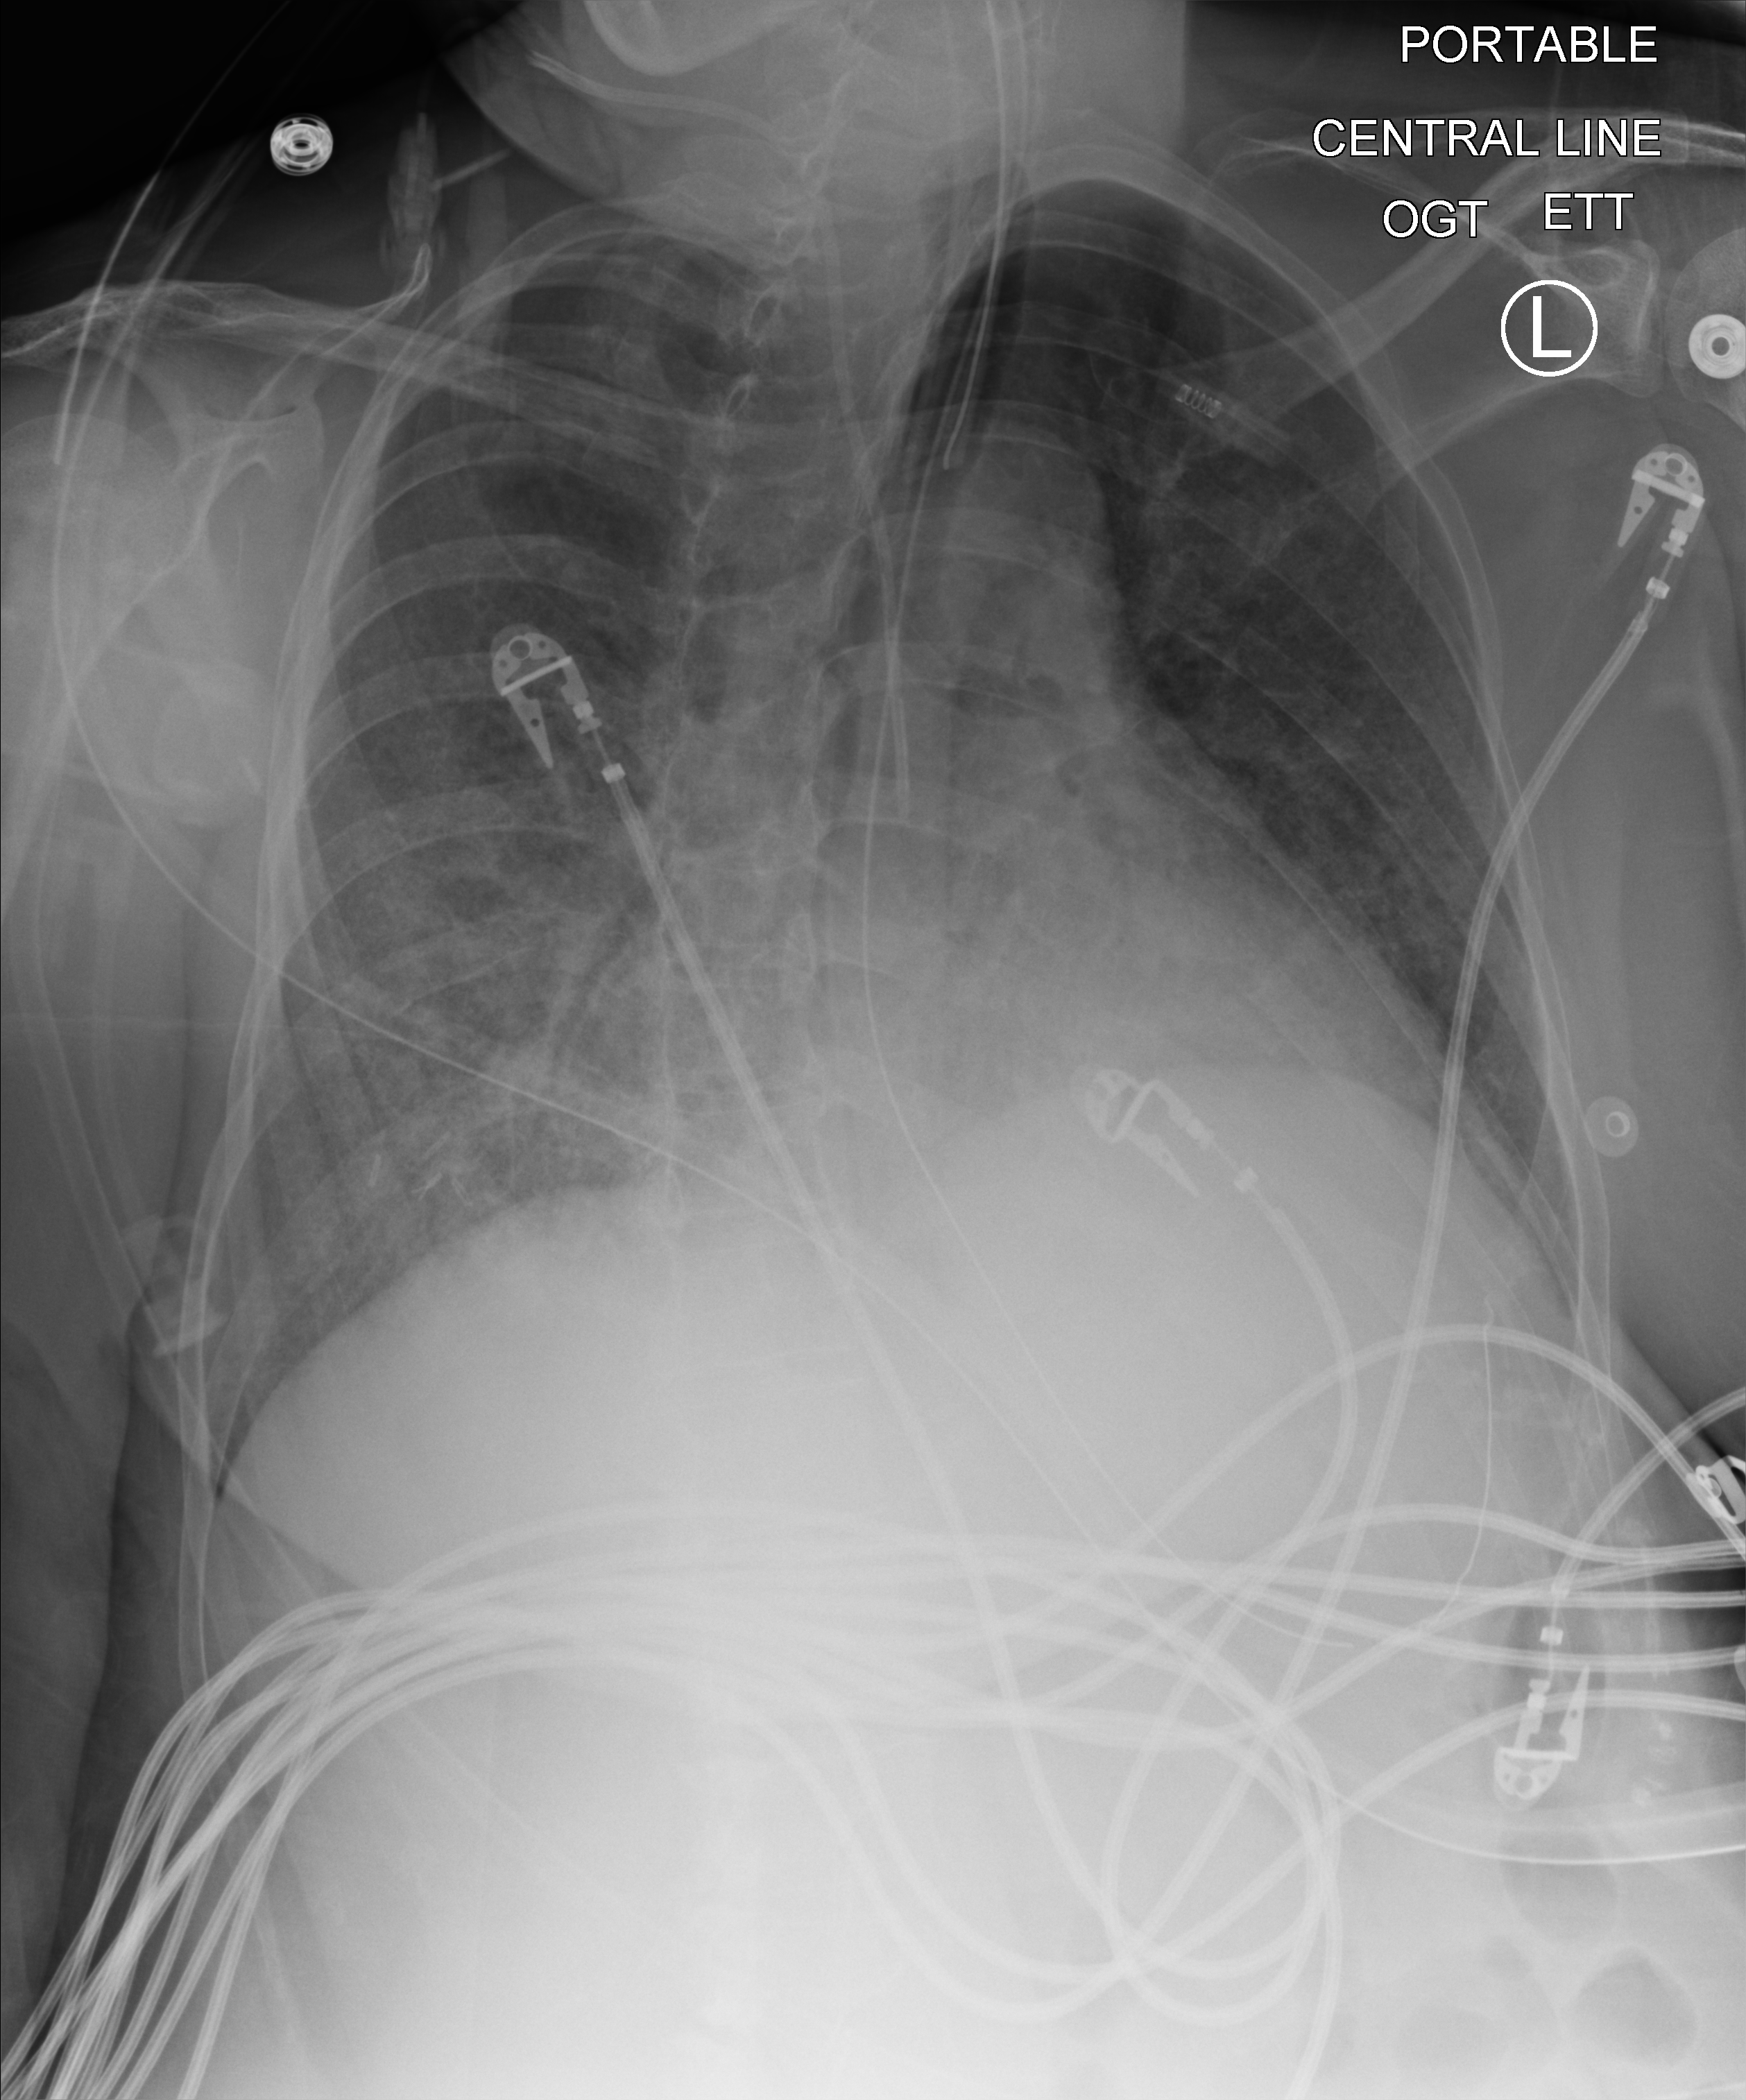
Bedside chest radiograph (computed radiography); anteroposterior (AP) projection. Female patient hospitalised with COVID-19, age 18–59 years.
Admission-level facts for this patient (not findings on this image; timing relative to this image not recorded):
- length of hospital stay: 21 days